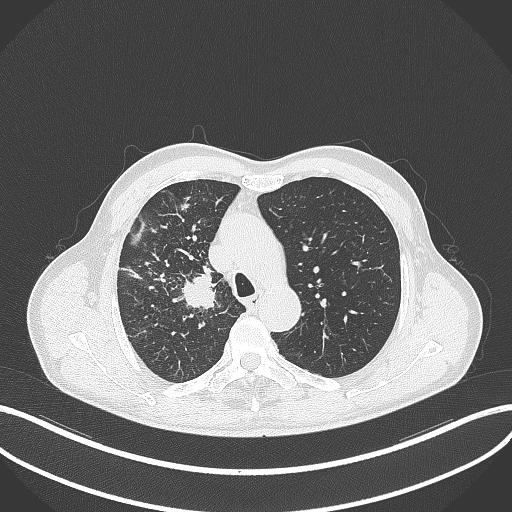
Chest CT, one axial slice. Position 351 of 490 along the scan axis. 120 kVp. Lung window (W 1500 / L -600 HU). 1 mm slice thickness. 512 × 512 image matrix, field of view 400 × 400 mm. Patient: male, 69 years. From the clinical record (not read from this slice): clinical TNM (as recorded): T2a N0 M0.
Outlined on this slice (rectangle marked by the reading radiologist):
- lung tumour (recorded histology: adenocarcinoma): bounding box [x1, y1, x2, y2] px = [176, 271, 218, 312]